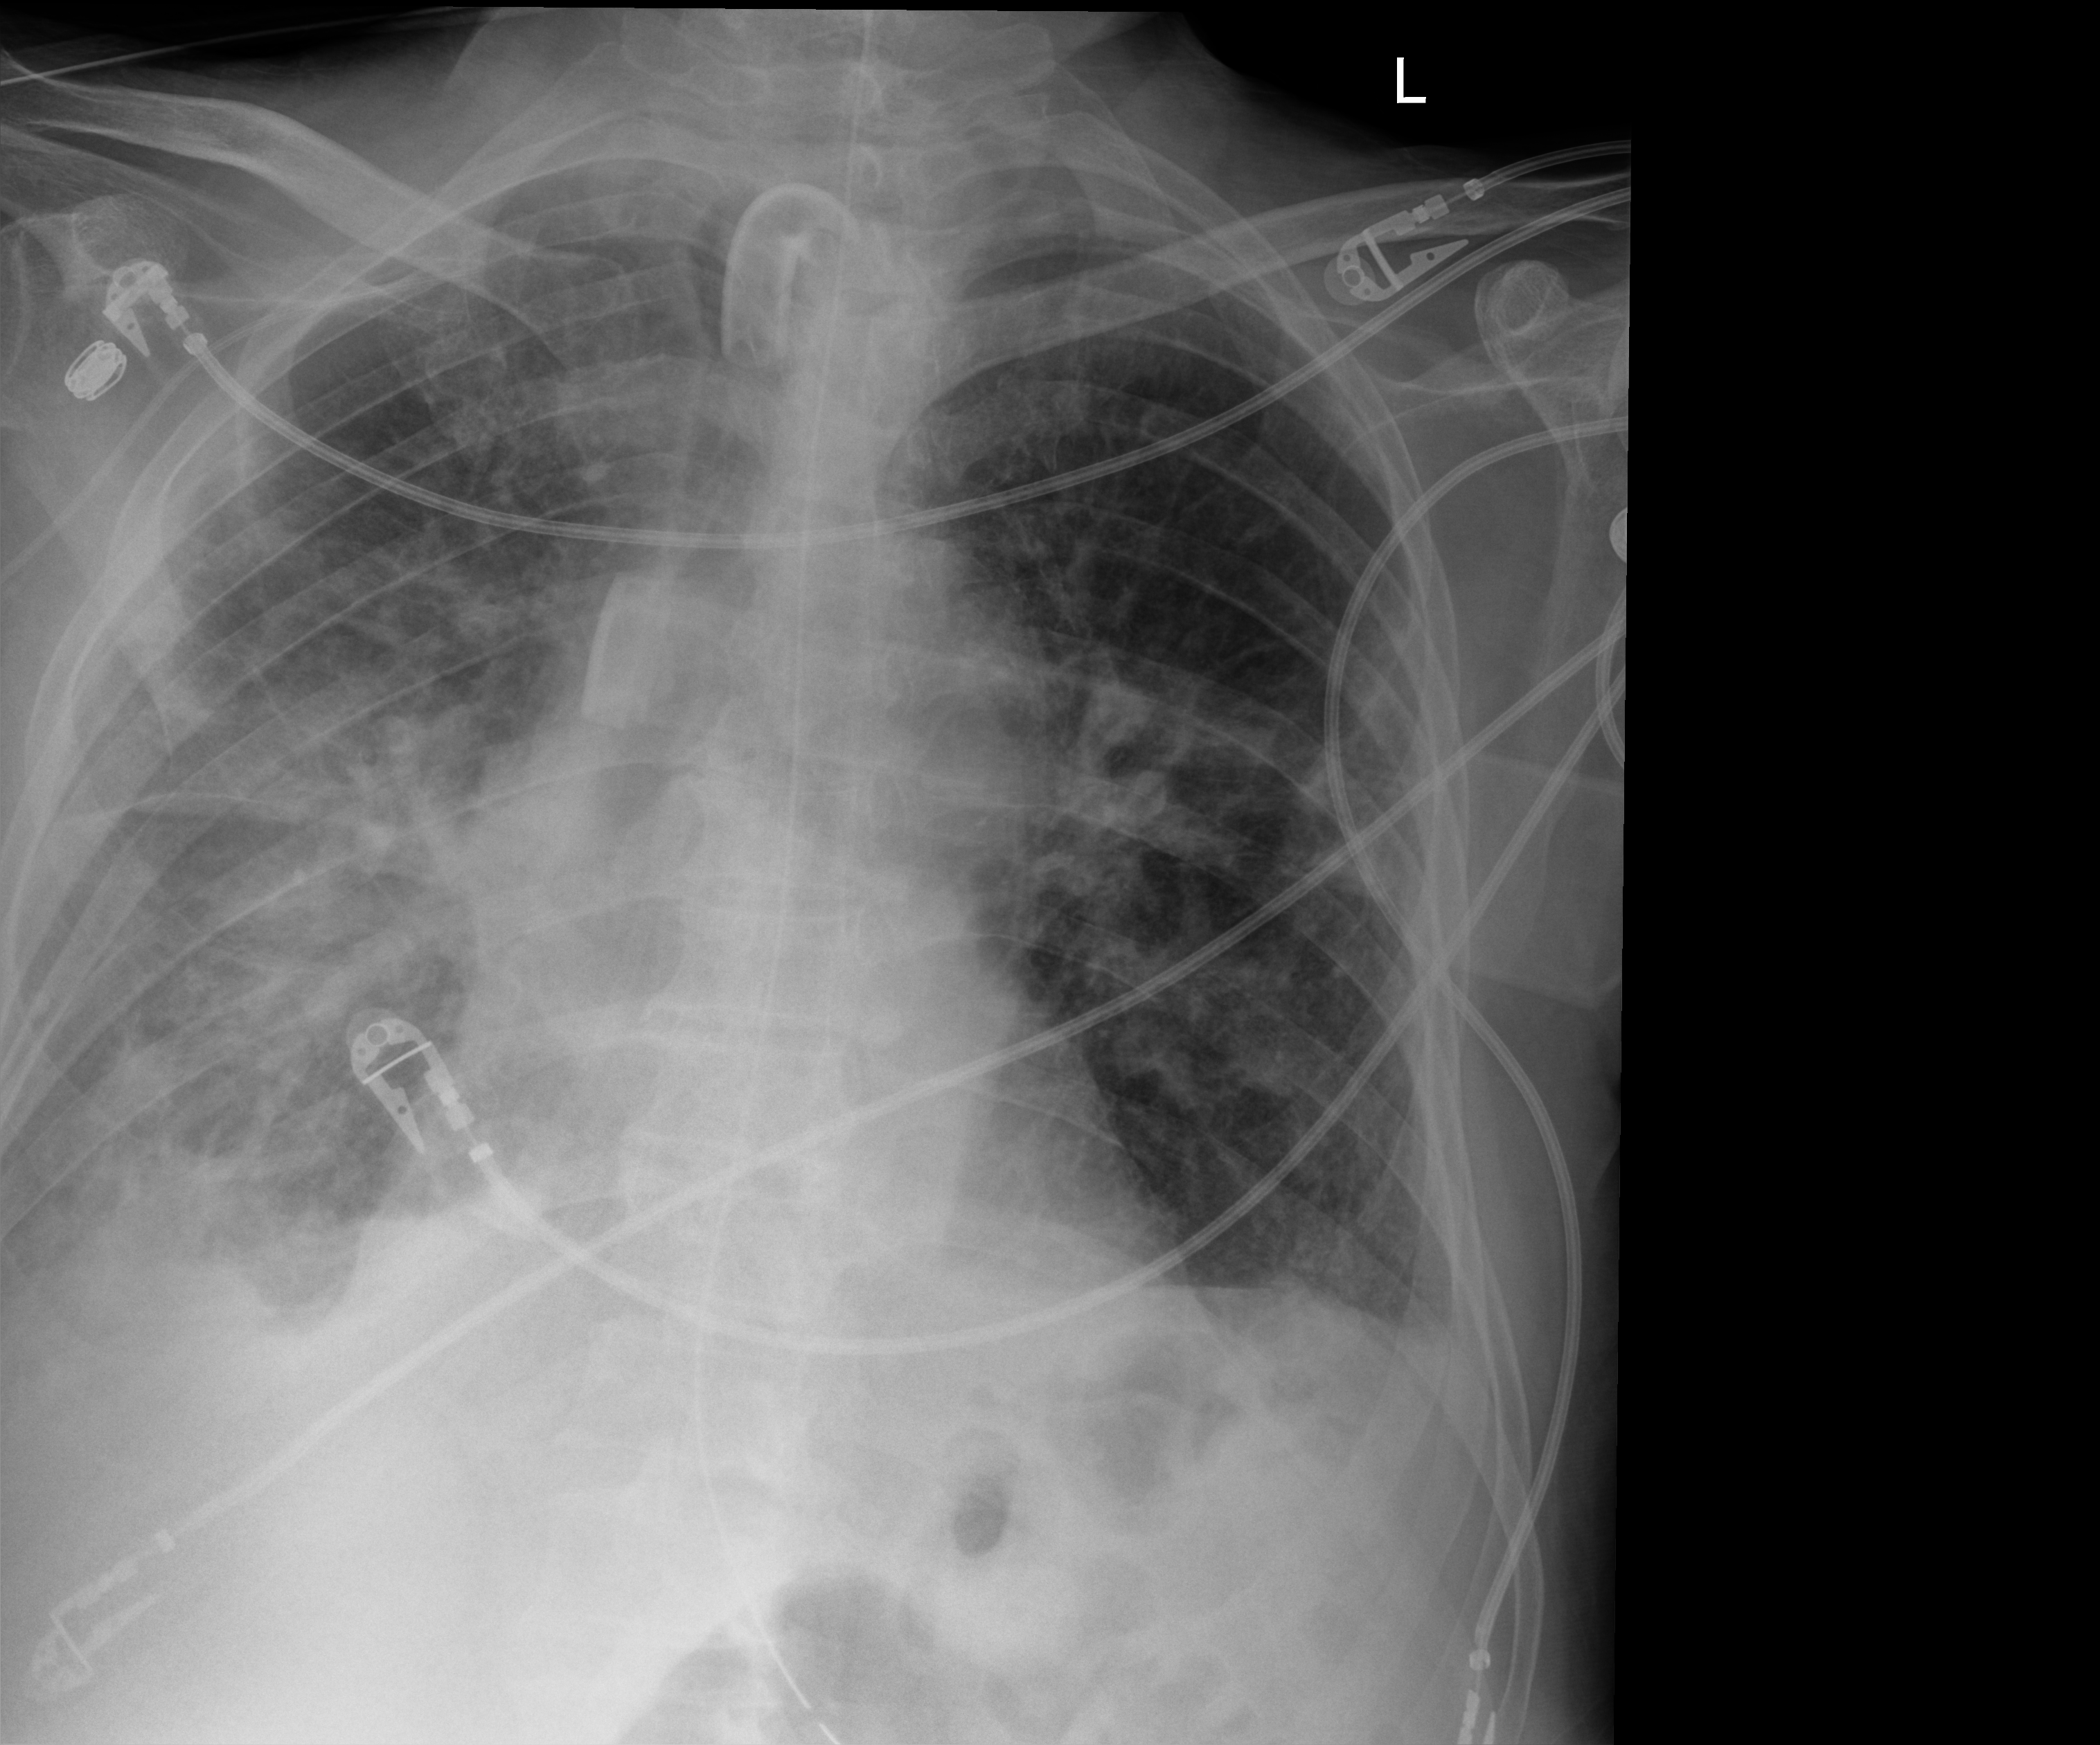
Chest X-ray (portable). Male patient hospitalised with COVID-19, age 75–90 years.
Admission-level facts for this patient (not findings on this image; timing relative to this image not recorded): COPD (admission record): no; mechanically ventilated during this hospital stay: yes; admitted to intensive care during this hospital stay: yes.